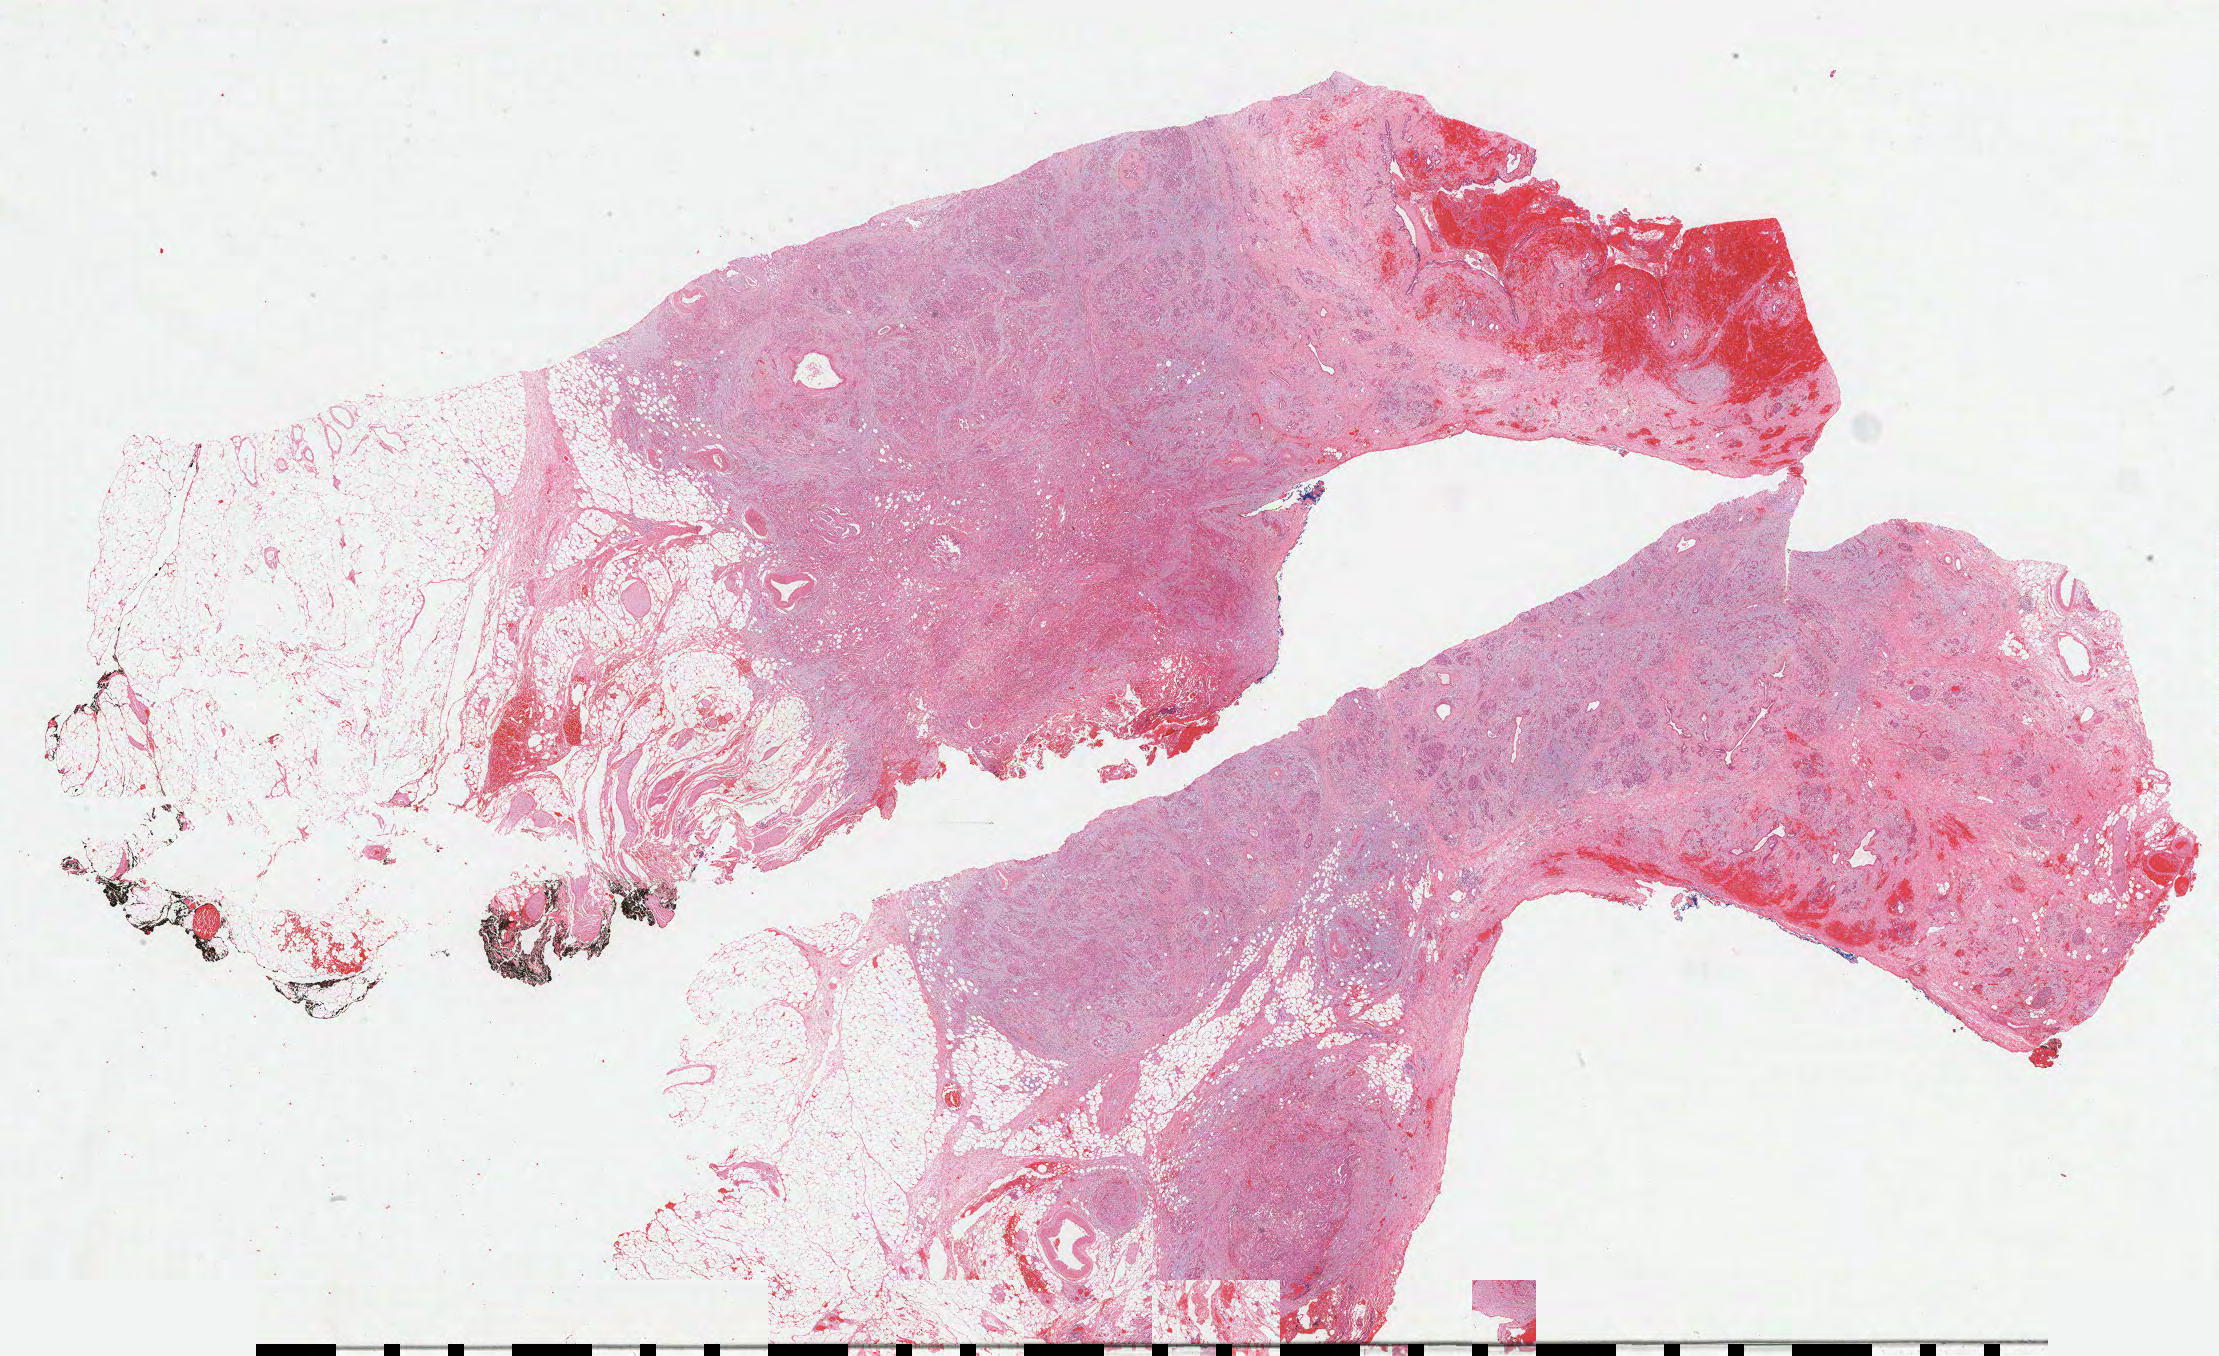
Whole-slide histology image, H&E — whole scanned area (about 35.9 x 21.9 mm, from a 40x scan) shown as a low-resolution overview, FFPE section, pancreas, primary tumour sample. Female, age 69 years at initial diagnosis. Histologic grade: G3 (poorly differentiated).
- AJCC pathologic stage: IIB (7th edition)
- pathologic diagnosis: Infiltrating duct carcinoma, NOS (head of pancreas)
- lymph nodes positive (case pathology): 5 of 21 examined